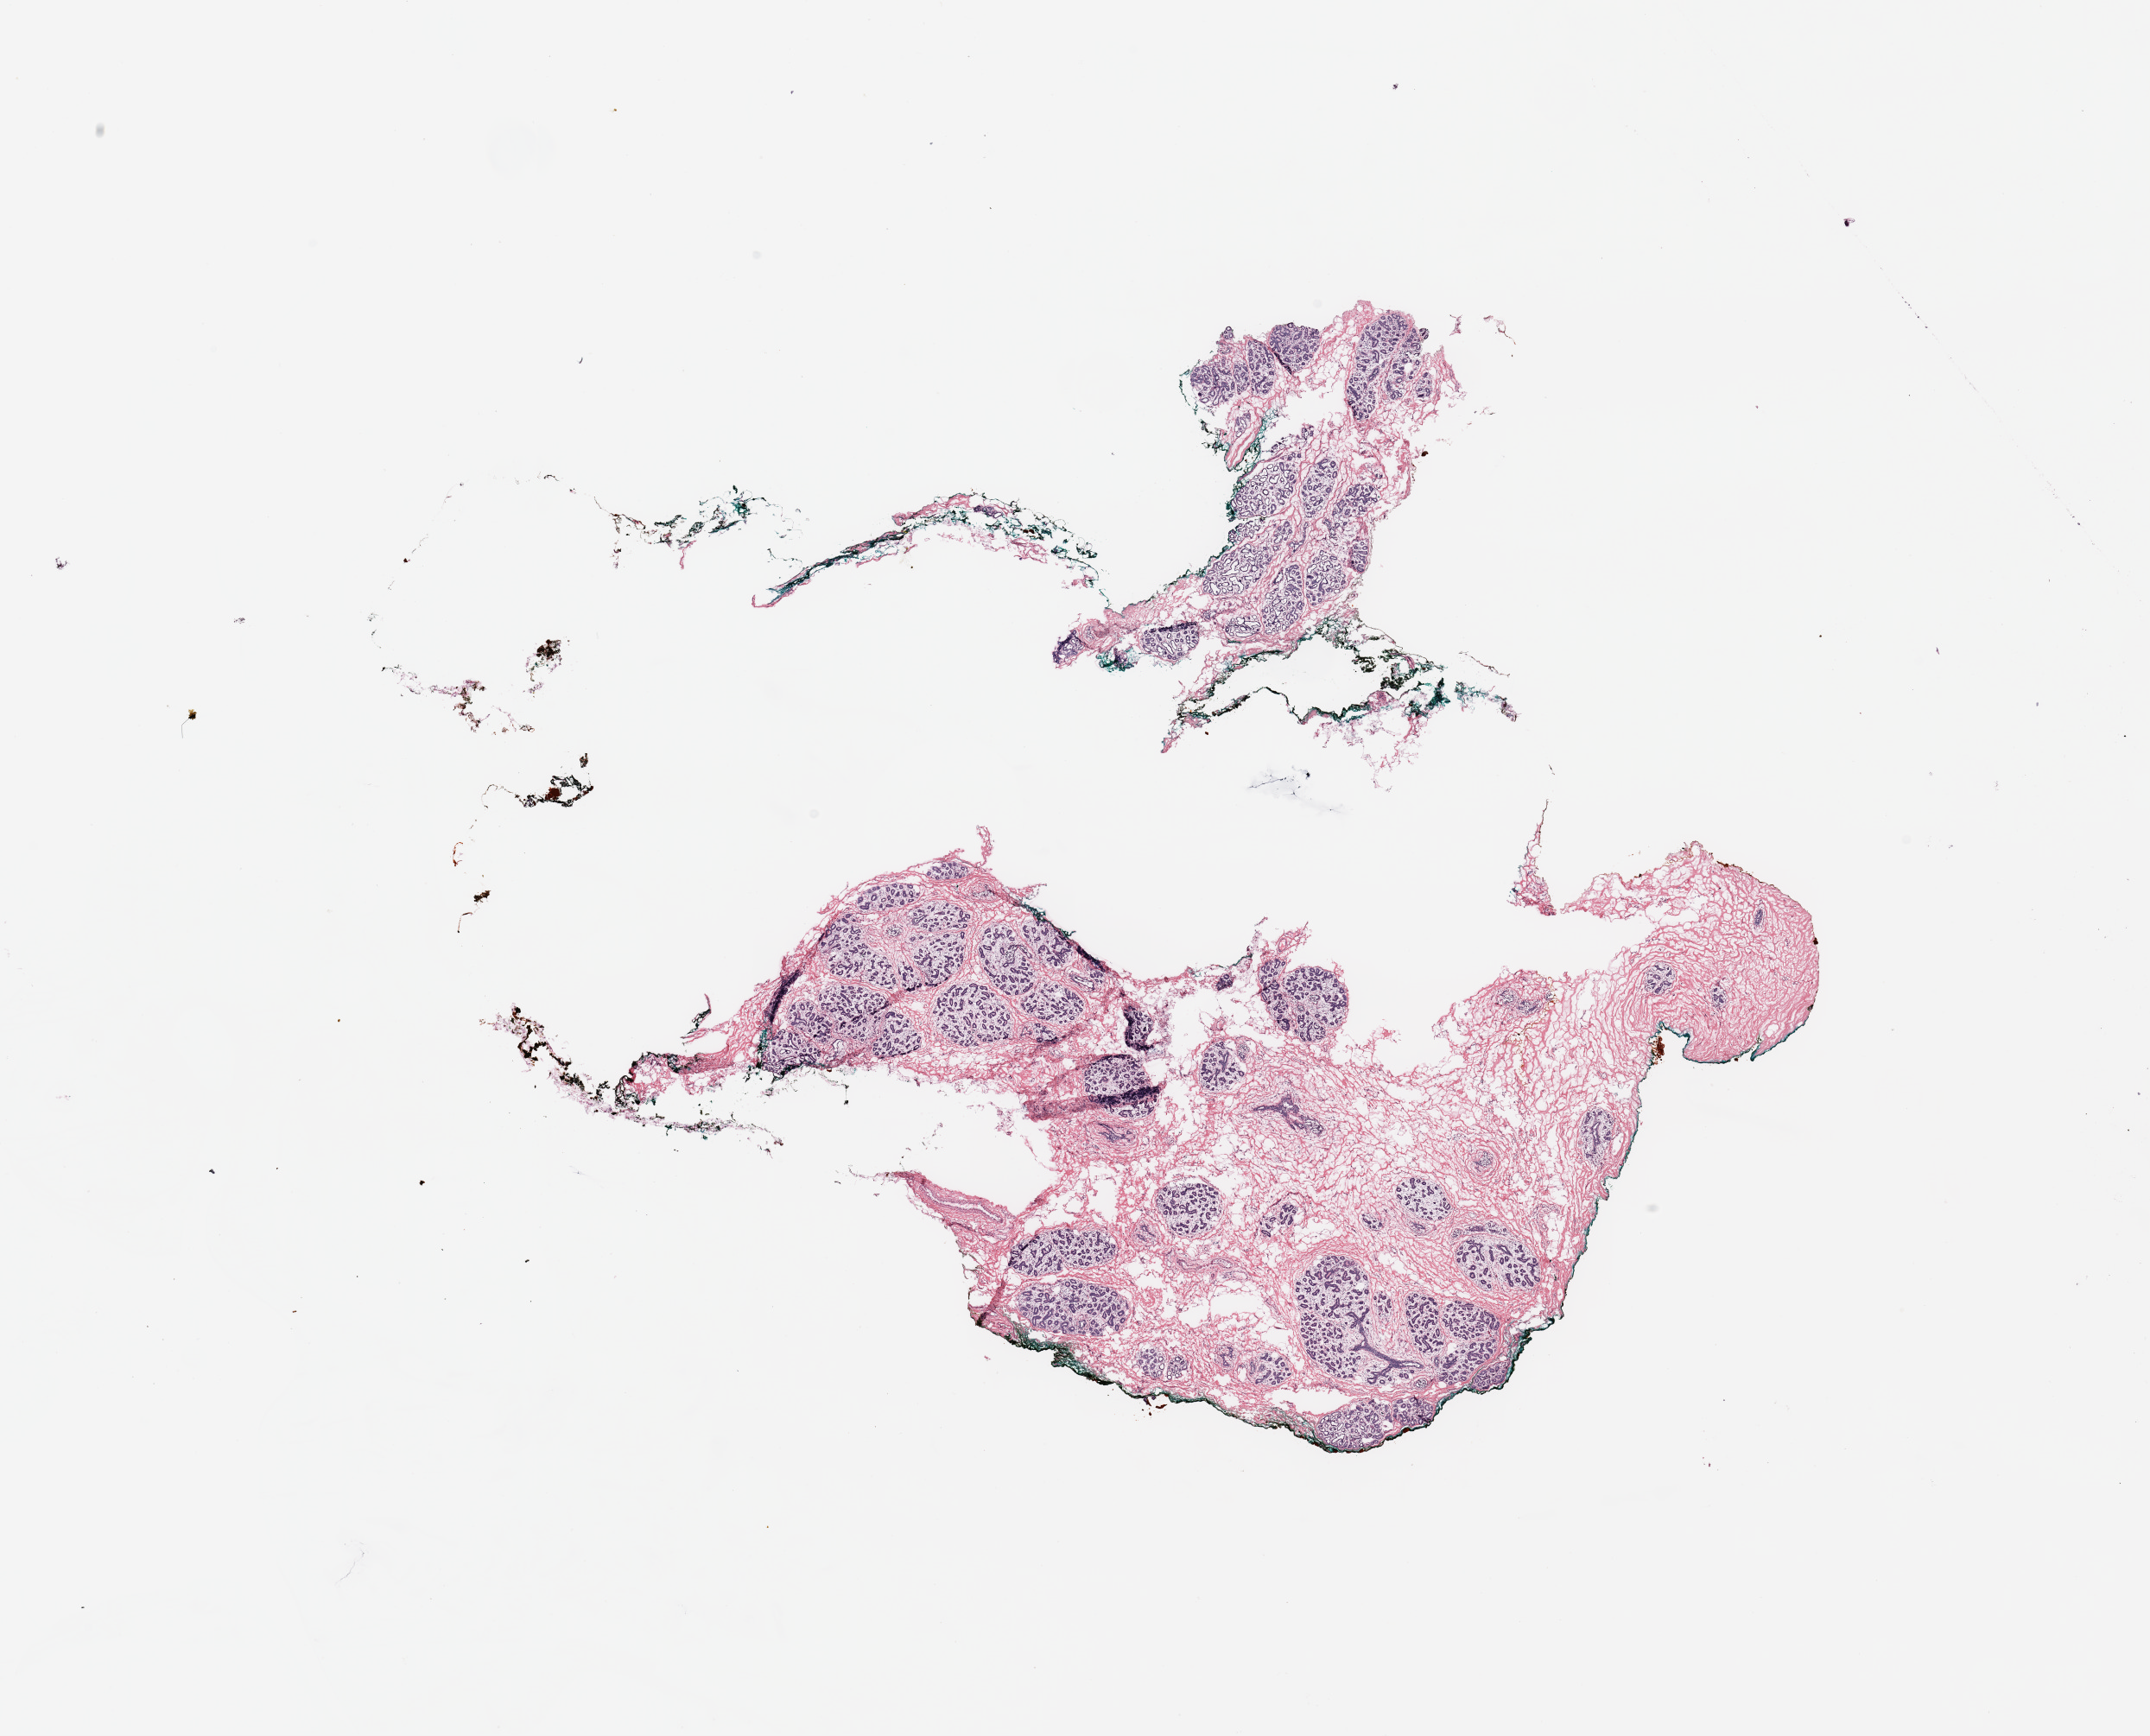
Whole-slide histology image, Hematoxylin and eosin (H&E) stained — shown as a low-resolution overview of the whole scanned area (about 19.7 x 15.9 mm); breast, tissue type not recorded.
Patient diagnosis (cohort enrolment): breast cancer (breast).